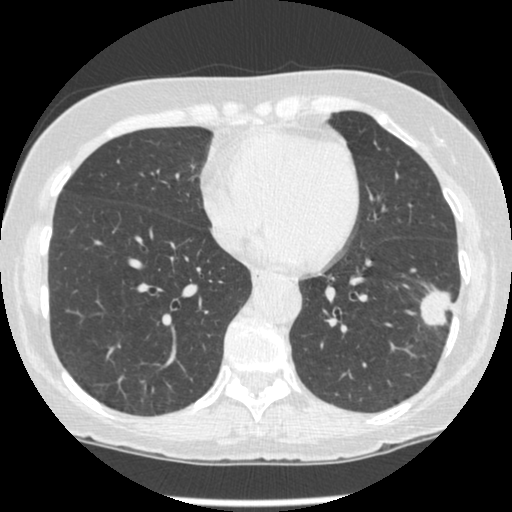
Low-dose screening chest CT, one axial slice; slice 93 of 247 in the series (ordered by position); reconstruction kernel STANDARD; 120 kVp; lung window (W 1500 / L -600 HU); 1.25 mm slice thickness; 512 × 512 image matrix.
Outlined on this slice (expert manual segmentation):
- lesion 1 (tumor, lower lobe of left lung): bounding box (x1, y1, x2, y2) in pixels: (420, 290, 454, 326)